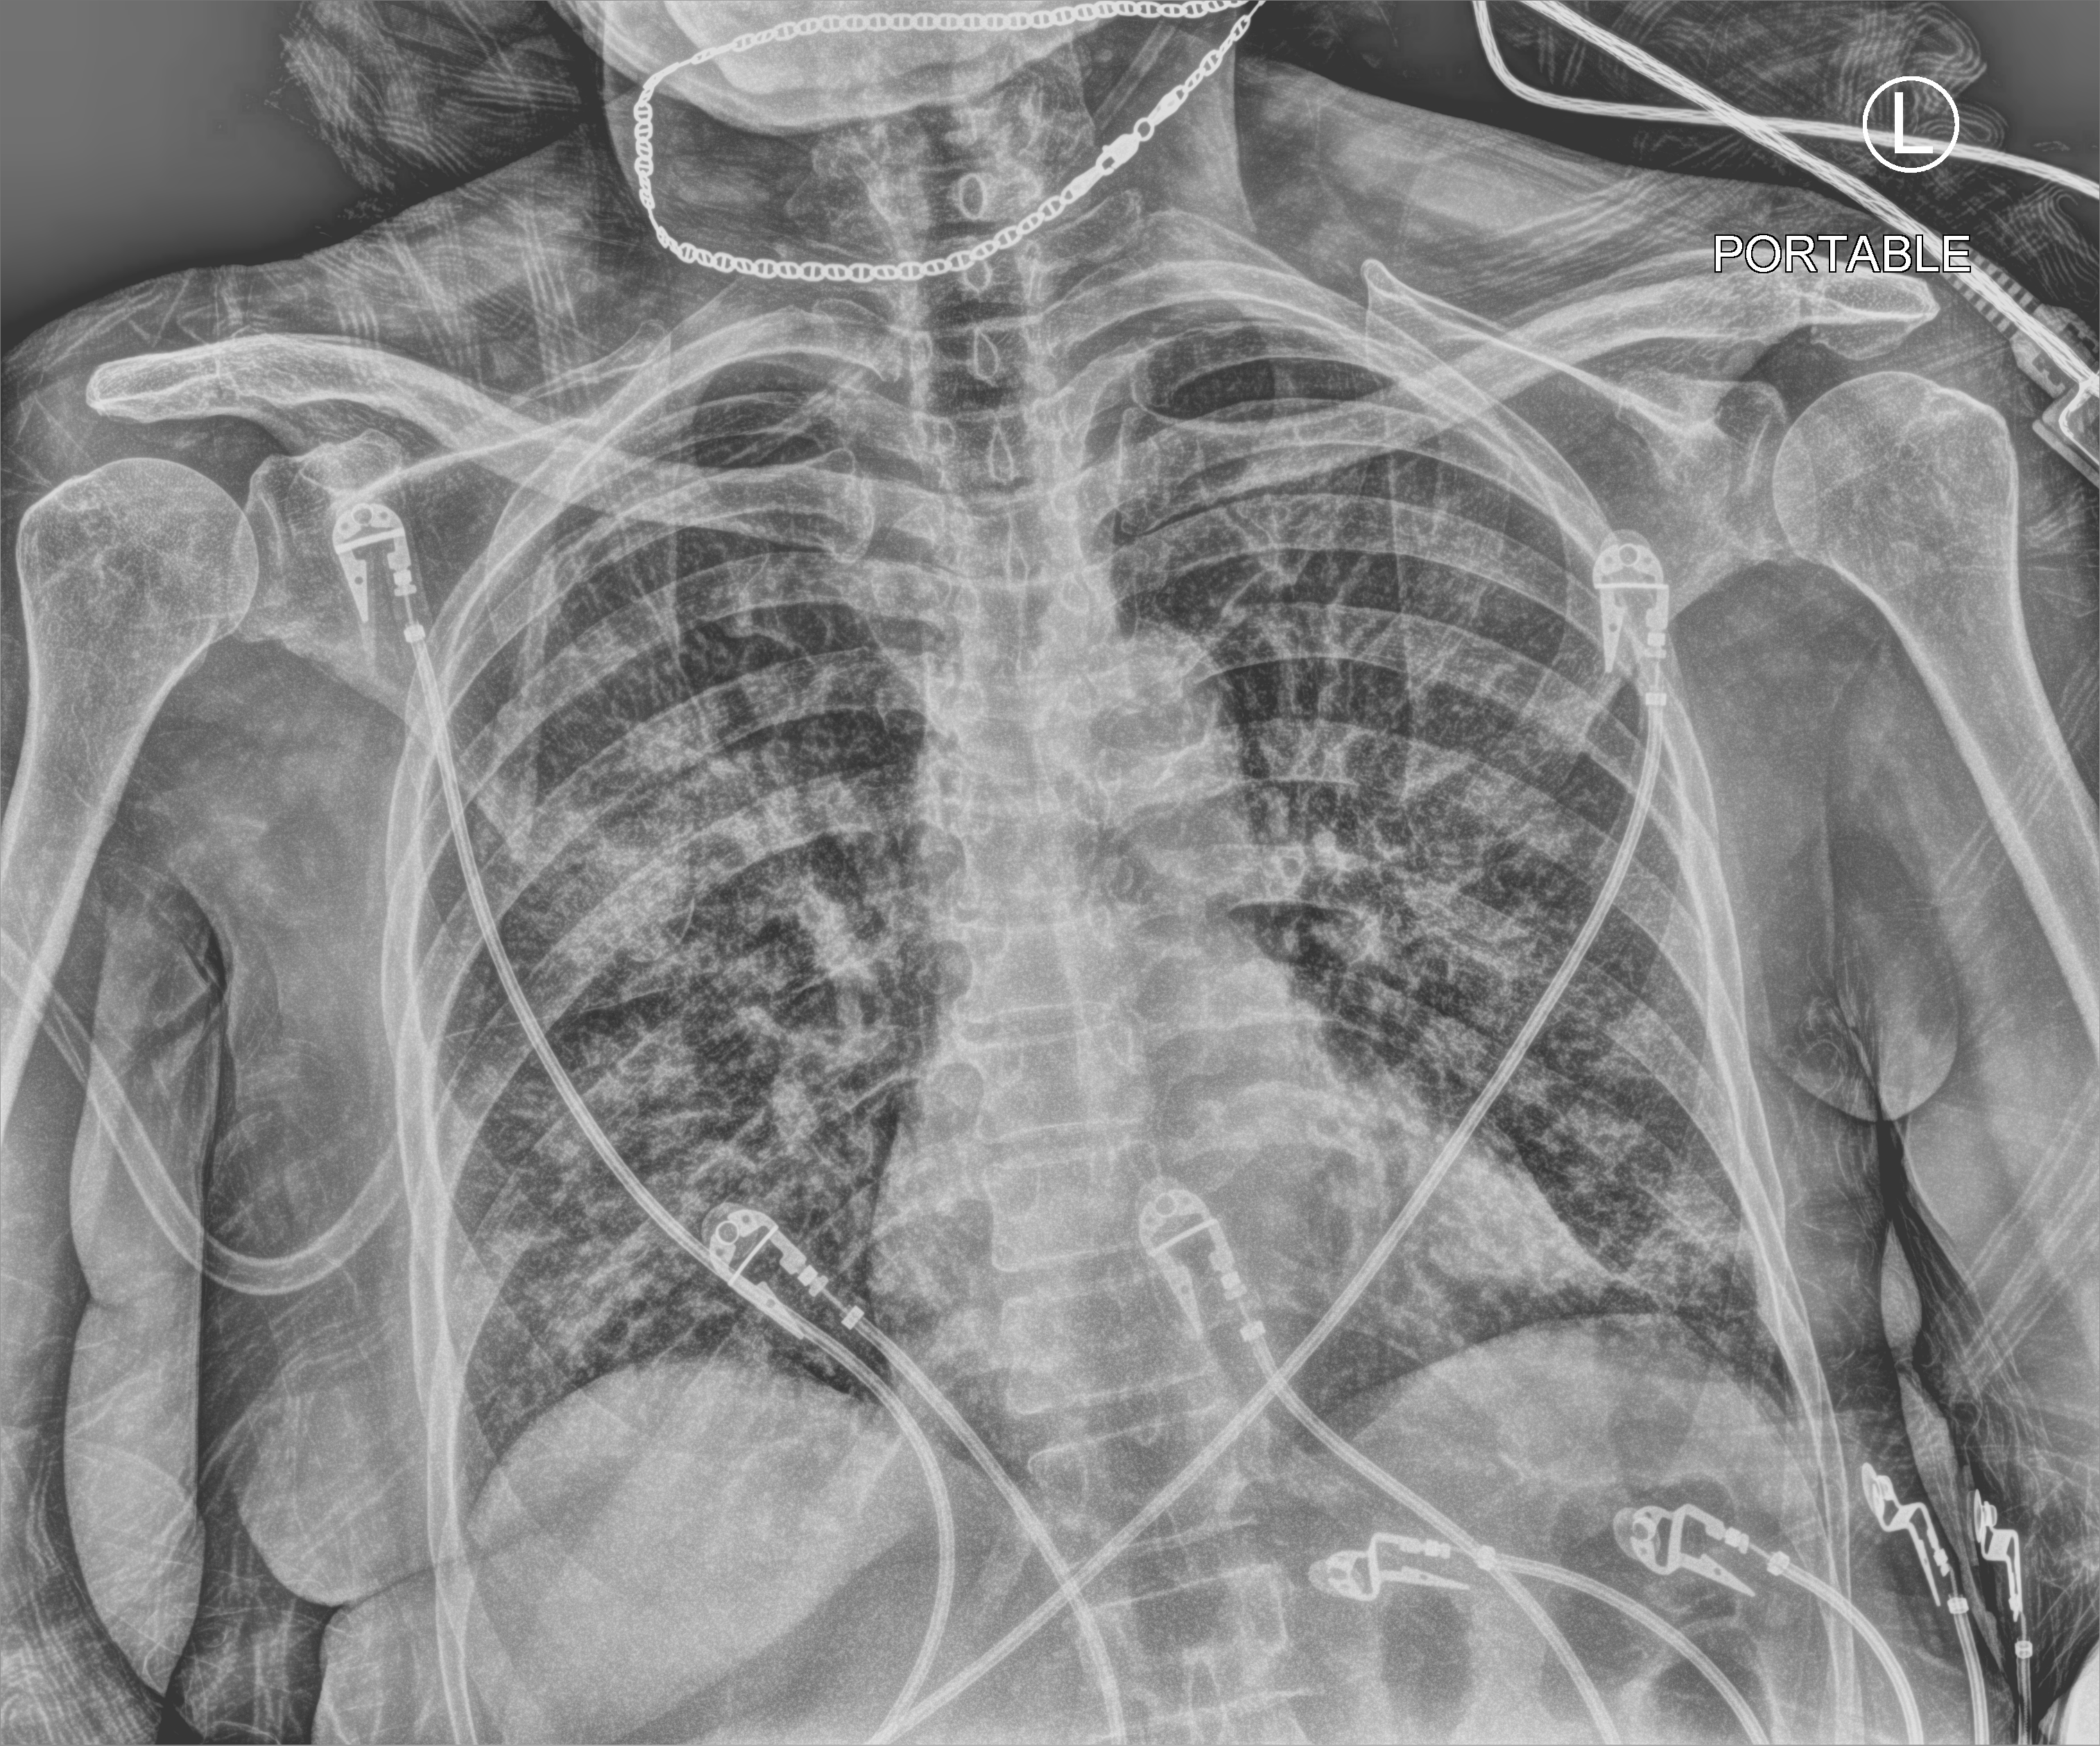
Bedside chest radiograph (computed radiography); anteroposterior (AP) projection. Female patient hospitalised with COVID-19, age 75–90 years.
Hospital-stay facts (about this admission, not read from this image; timing relative to this image not recorded):
- COPD (admission record): no